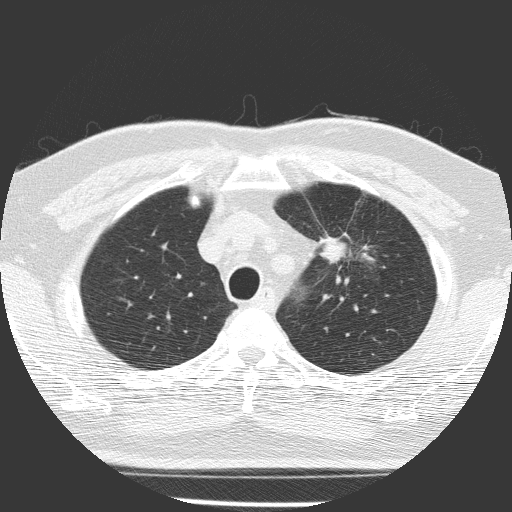
Low-dose screening chest CT, axial slice; first (baseline) screen; lung window (W 1500 / L -600 HU); 2 mm slice thickness; lung (sharp) reconstruction kernel (FC51); slice 36 of 156 in the series; 512 × 512 image matrix, field of view 309 × 309 mm. Male, age 70 years at enrolment. Current smoker at enrolment.
Lesion marked by an expert reader, box from (x=296, y=218) to (x=372, y=291) px. The screening reader recorded 3 non-calcified nodules or masses ≥4 mm on this exam (left upper lobe, left lower lobe, left upper lobe); which of them this box marks is not recorded. Lung cancer was diagnosed 58 days after this screen: squamous cell carcinoma, NOS, left upper lobe, poorly differentiated (G3), stage IB (AJCC 6th edition), 47 mm at pathology.